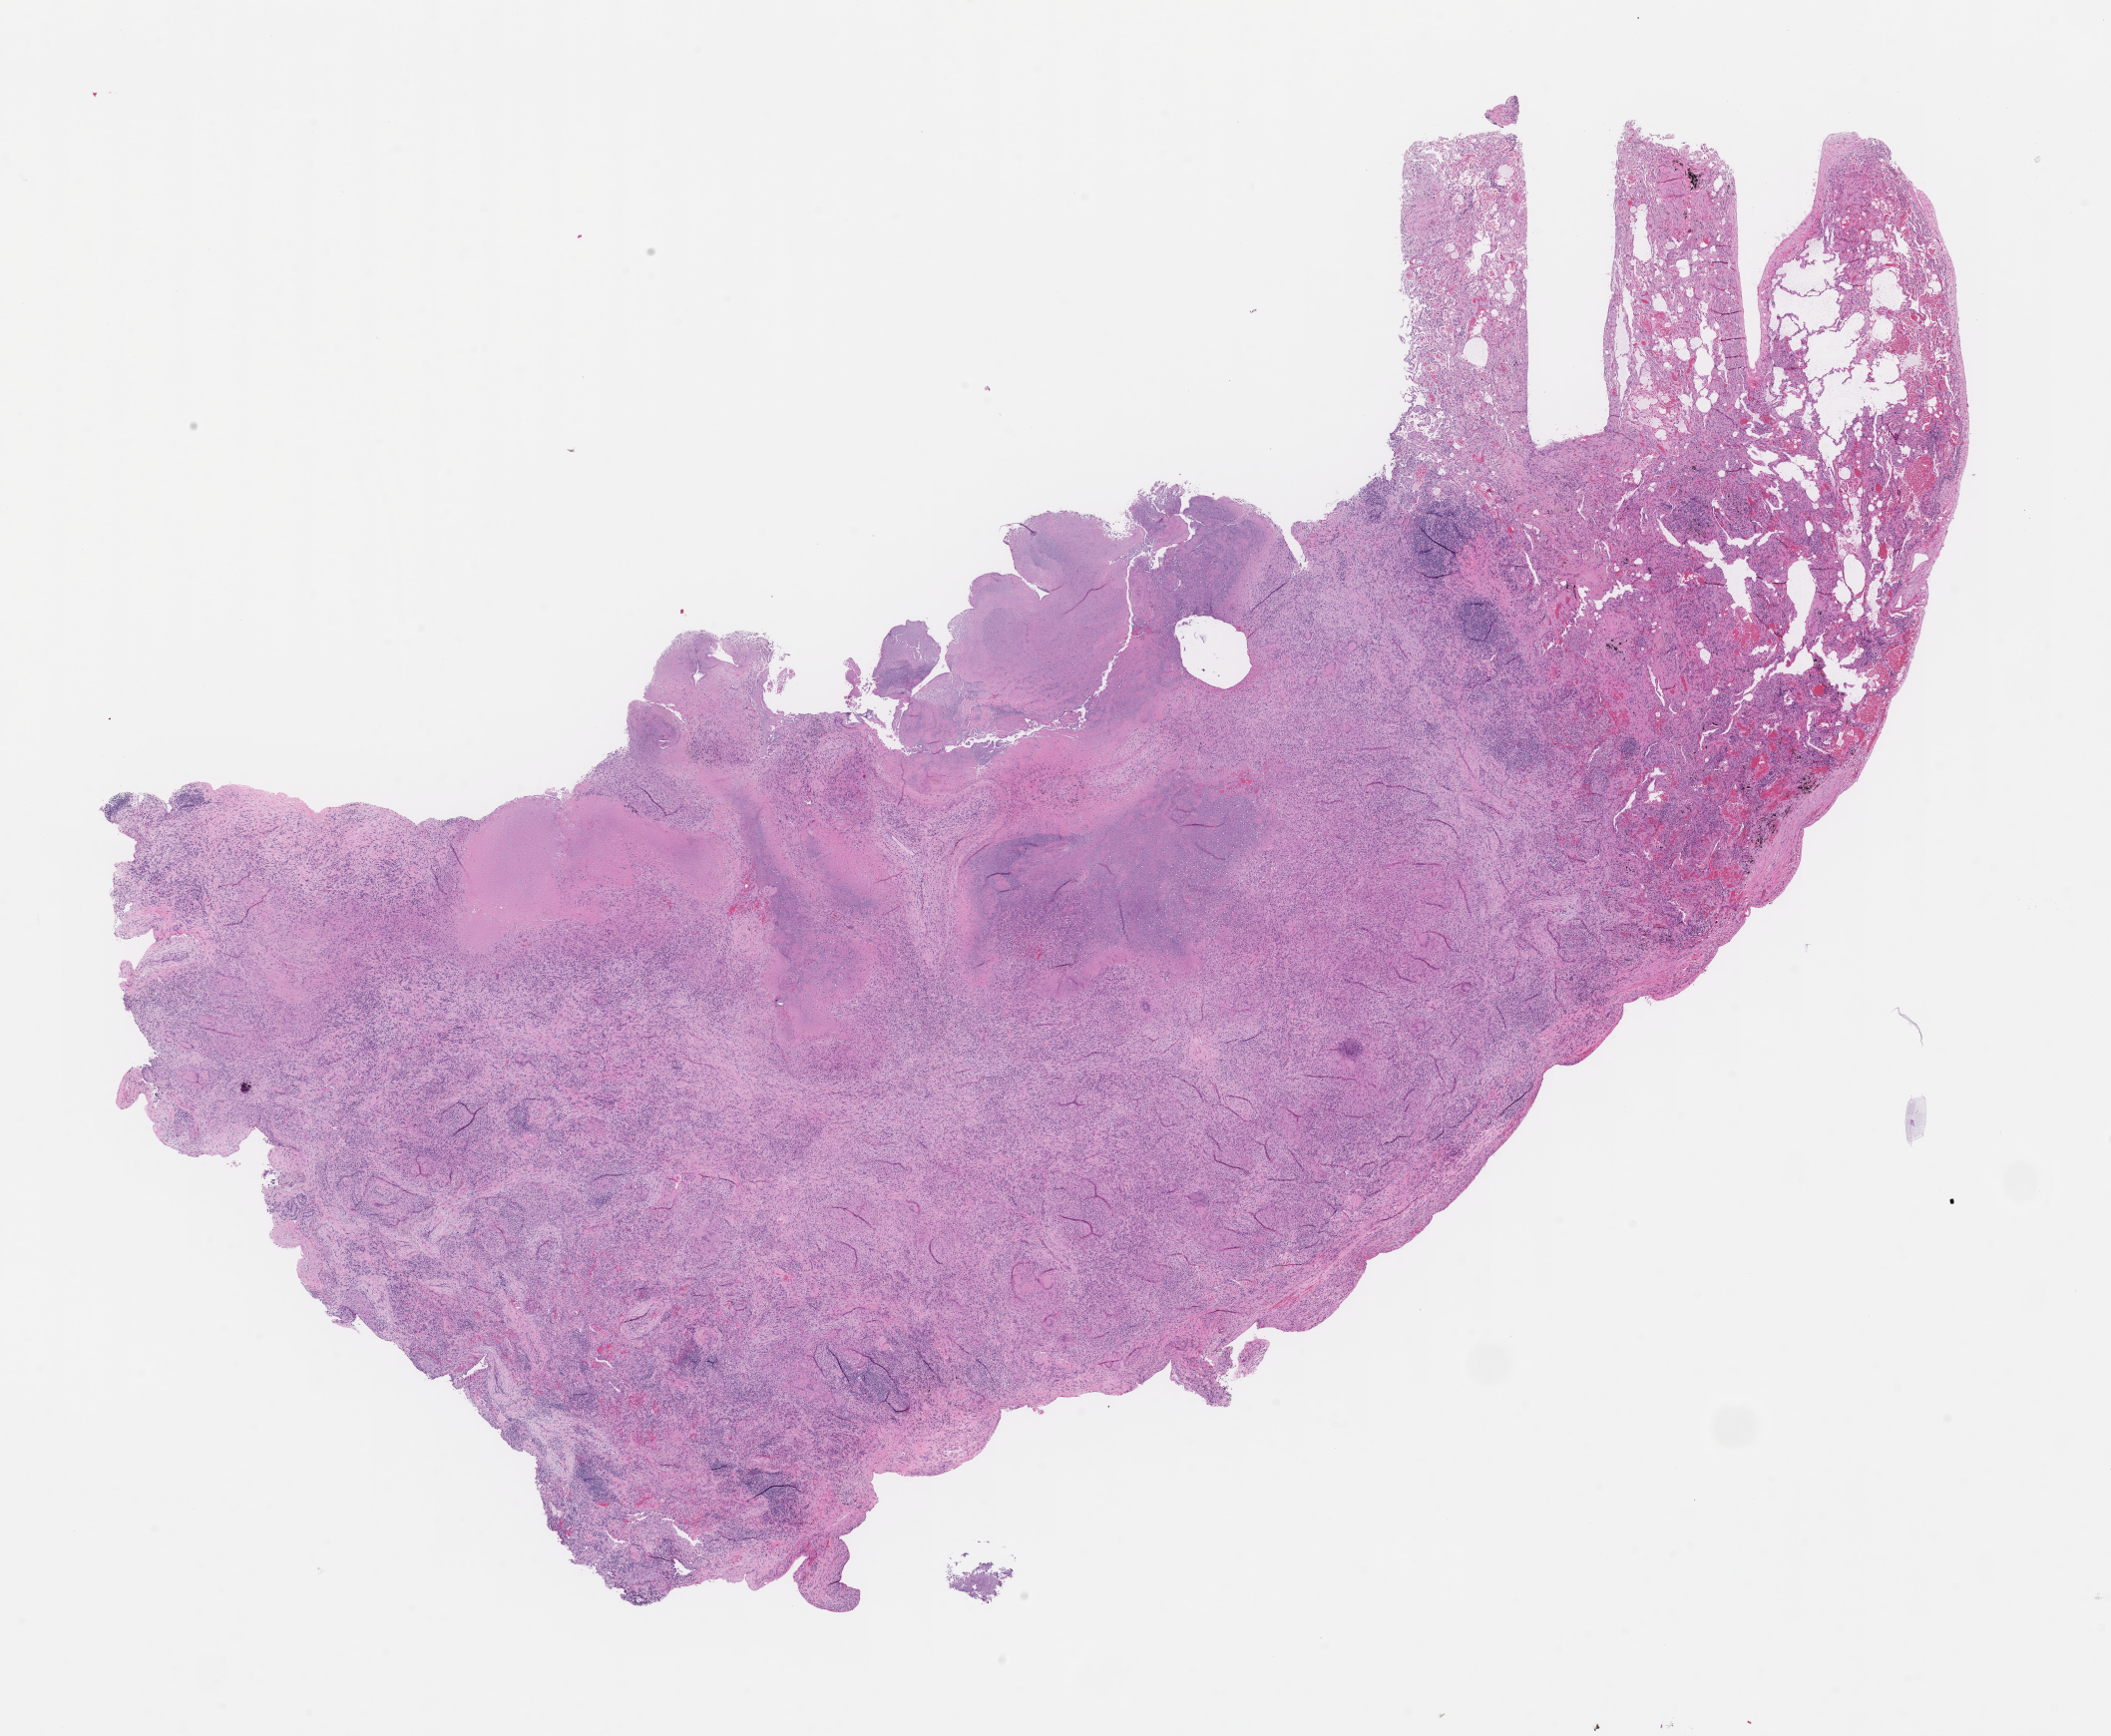
Digitized hematoxylin and eosin (H&E)-stained section, whole scanned area (about 17.1 x 14.1 mm) shown as a low-resolution overview. Formalin-fixed, paraffin-embedded (FFPE) tissue. Tissue site: lung. Collected at baseline (before treatment). Patient: male.
* this section: primary tumour tissue
* diagnosis: Non-Small Cell Lung Carcinoma